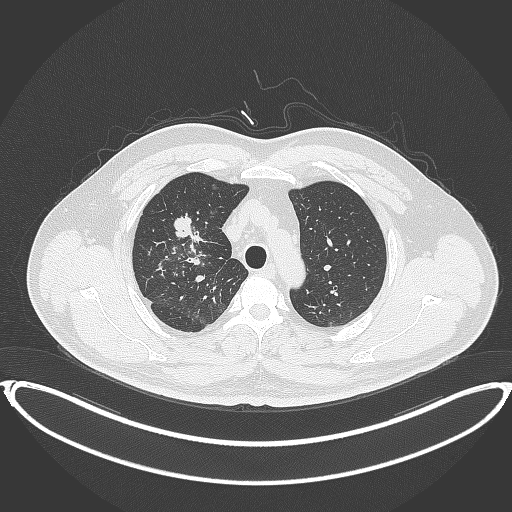
Chest CT, one axial slice. Position 300 of 399 along the scan axis. 120 kVp. Lung window (W 1500 / L -600 HU). 1 mm slice thickness. 512 × 512 image matrix, field of view 445 × 445 mm. Patient: male, 53 years. From the clinical record (not read from this slice): clinical TNM (as recorded): T2a N0 M0.
Outlined on this slice (rectangle marked by the reading radiologist):
- lung tumour (recorded histology: adenocarcinoma): box from (x=172, y=214) to (x=199, y=245) px